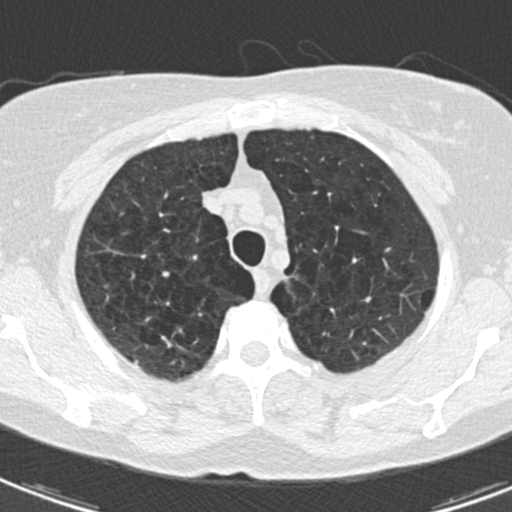
Low-dose screening chest CT, one axial slice. Slice 146 of 174 in the series (ordered by position). 120 kVp. Lung window (W 1500 / L -600 HU). 512 × 512 image matrix.
Structures marked on this image (manually delineated by an expert):
- lesion 1 (tumor, upper lobe of right lung): box from (x=161, y=335) to (x=172, y=348) px